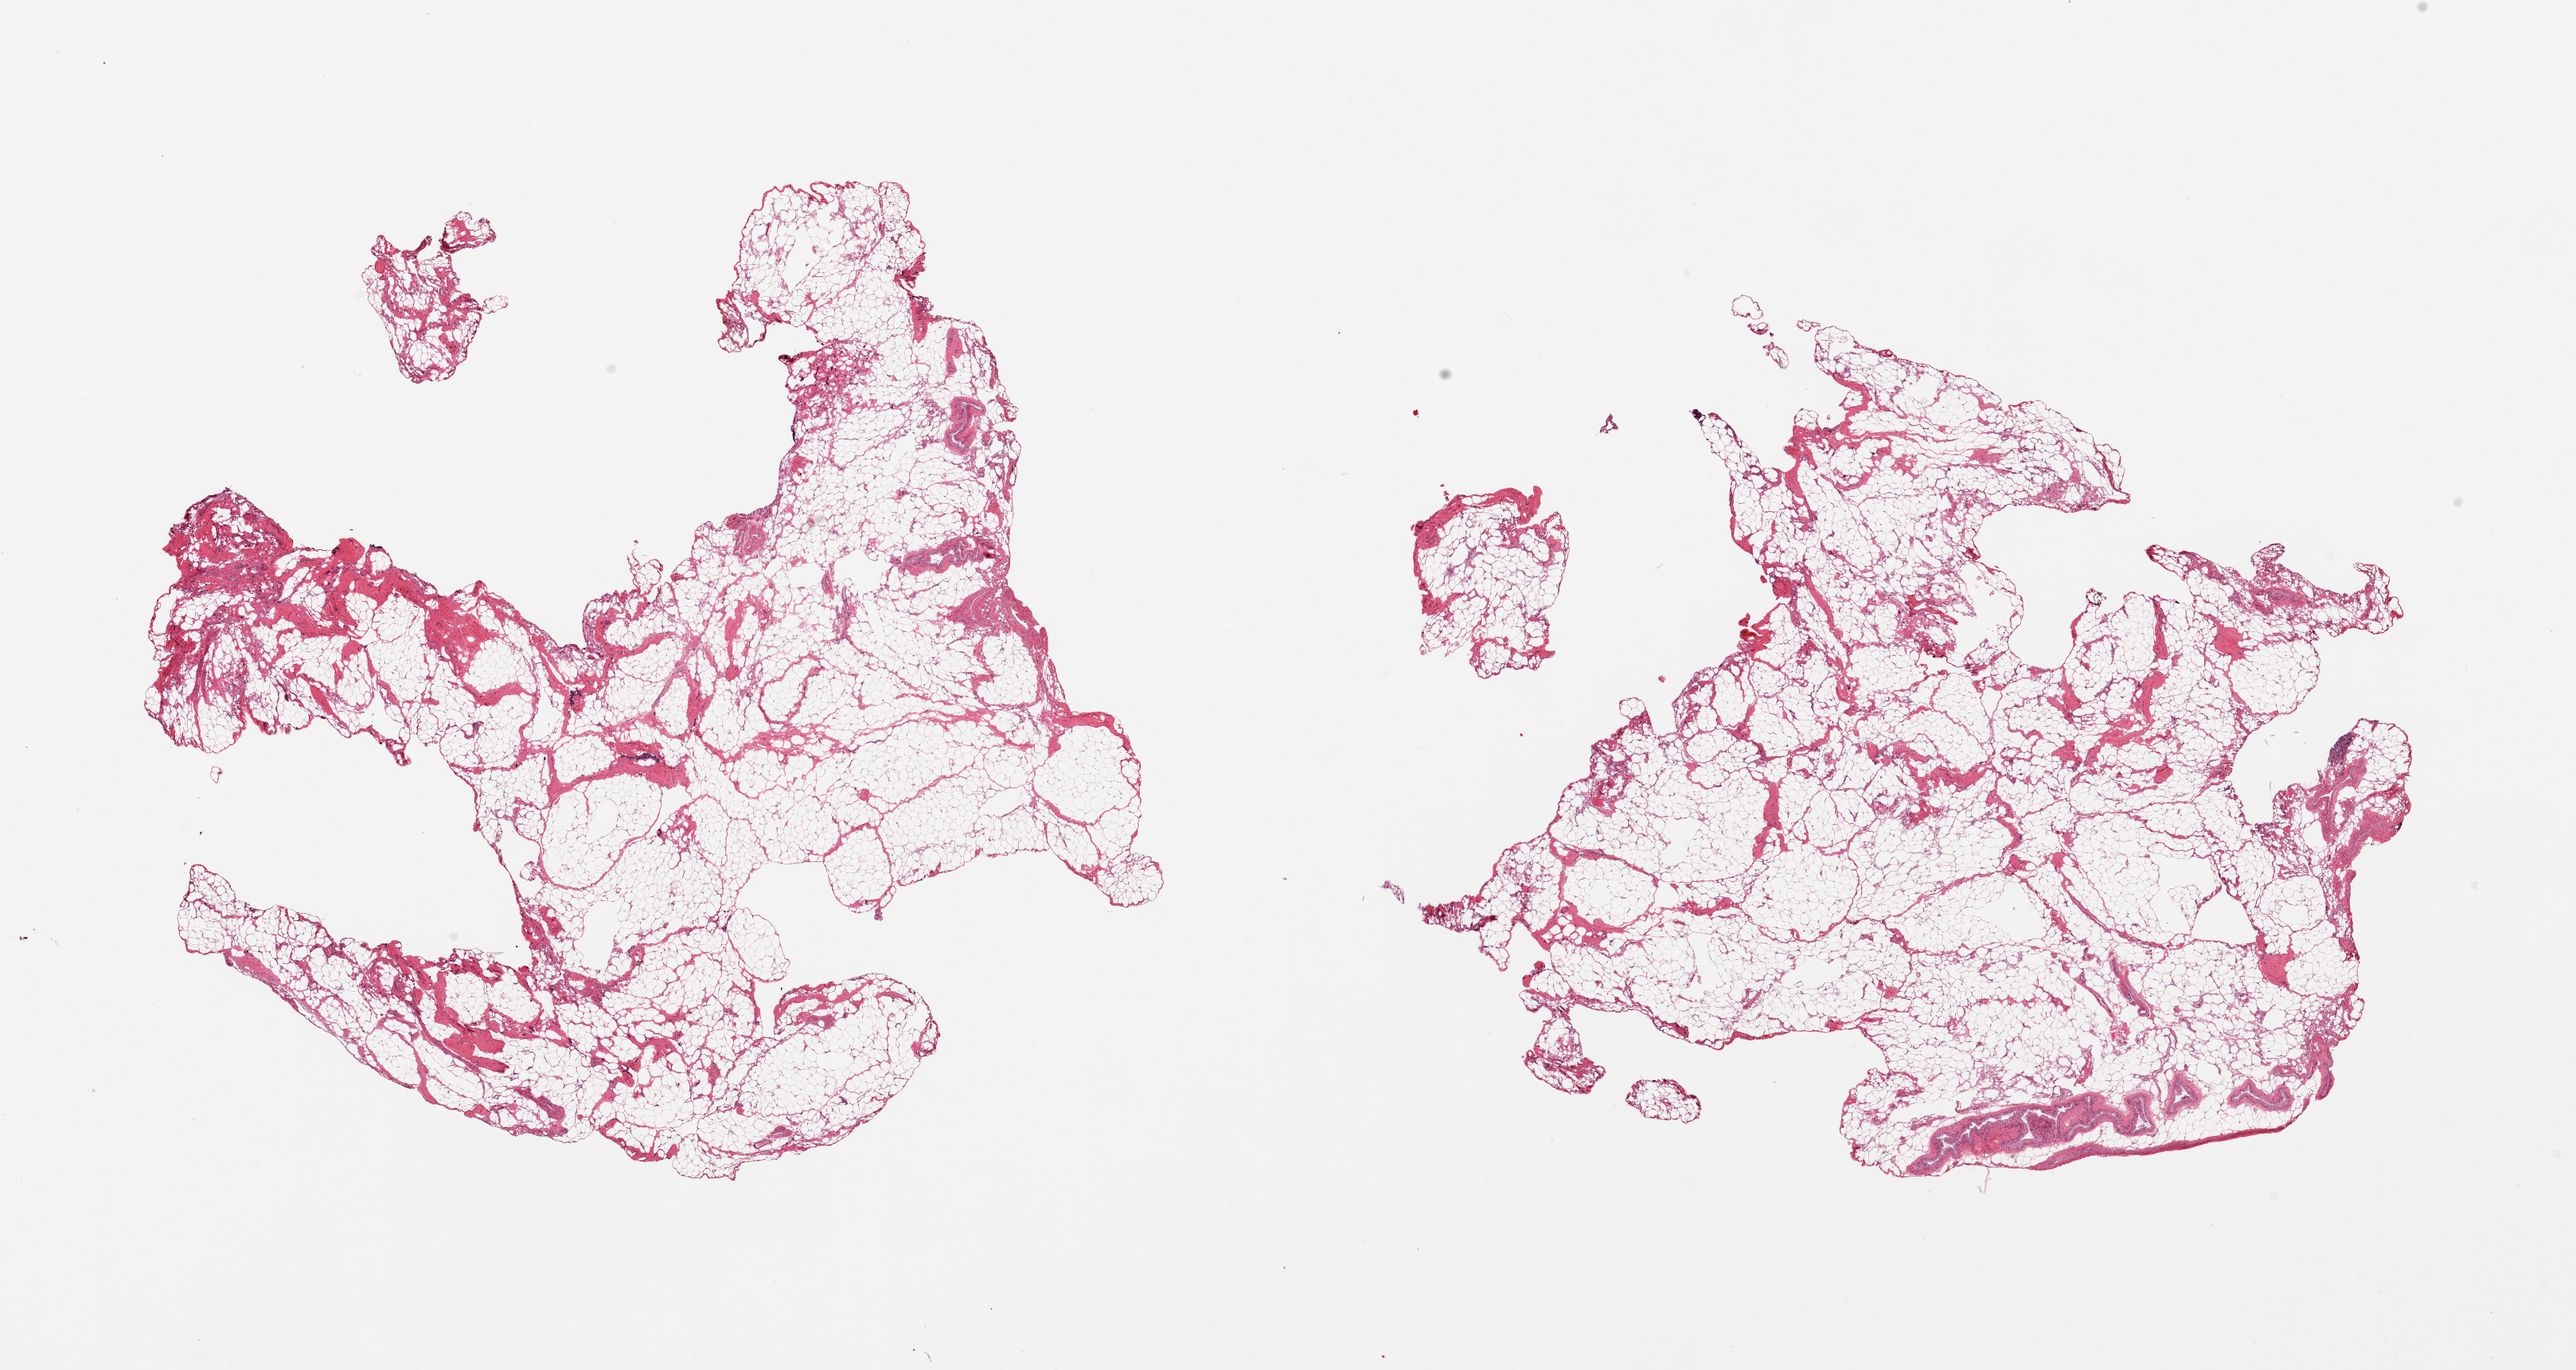
Whole-slide image, H&E stain — whole scanned area (about 25.6 x 13.6 mm) shown as a low-resolution overview; PAXgene-fixed, paraffin-embedded tissue; section of omentum (target tissue); donor tissue sample. Donor sex: male.
- reviewer comment on this tissue sample: 2 pieces, ~15% fibrous/vascular tissue